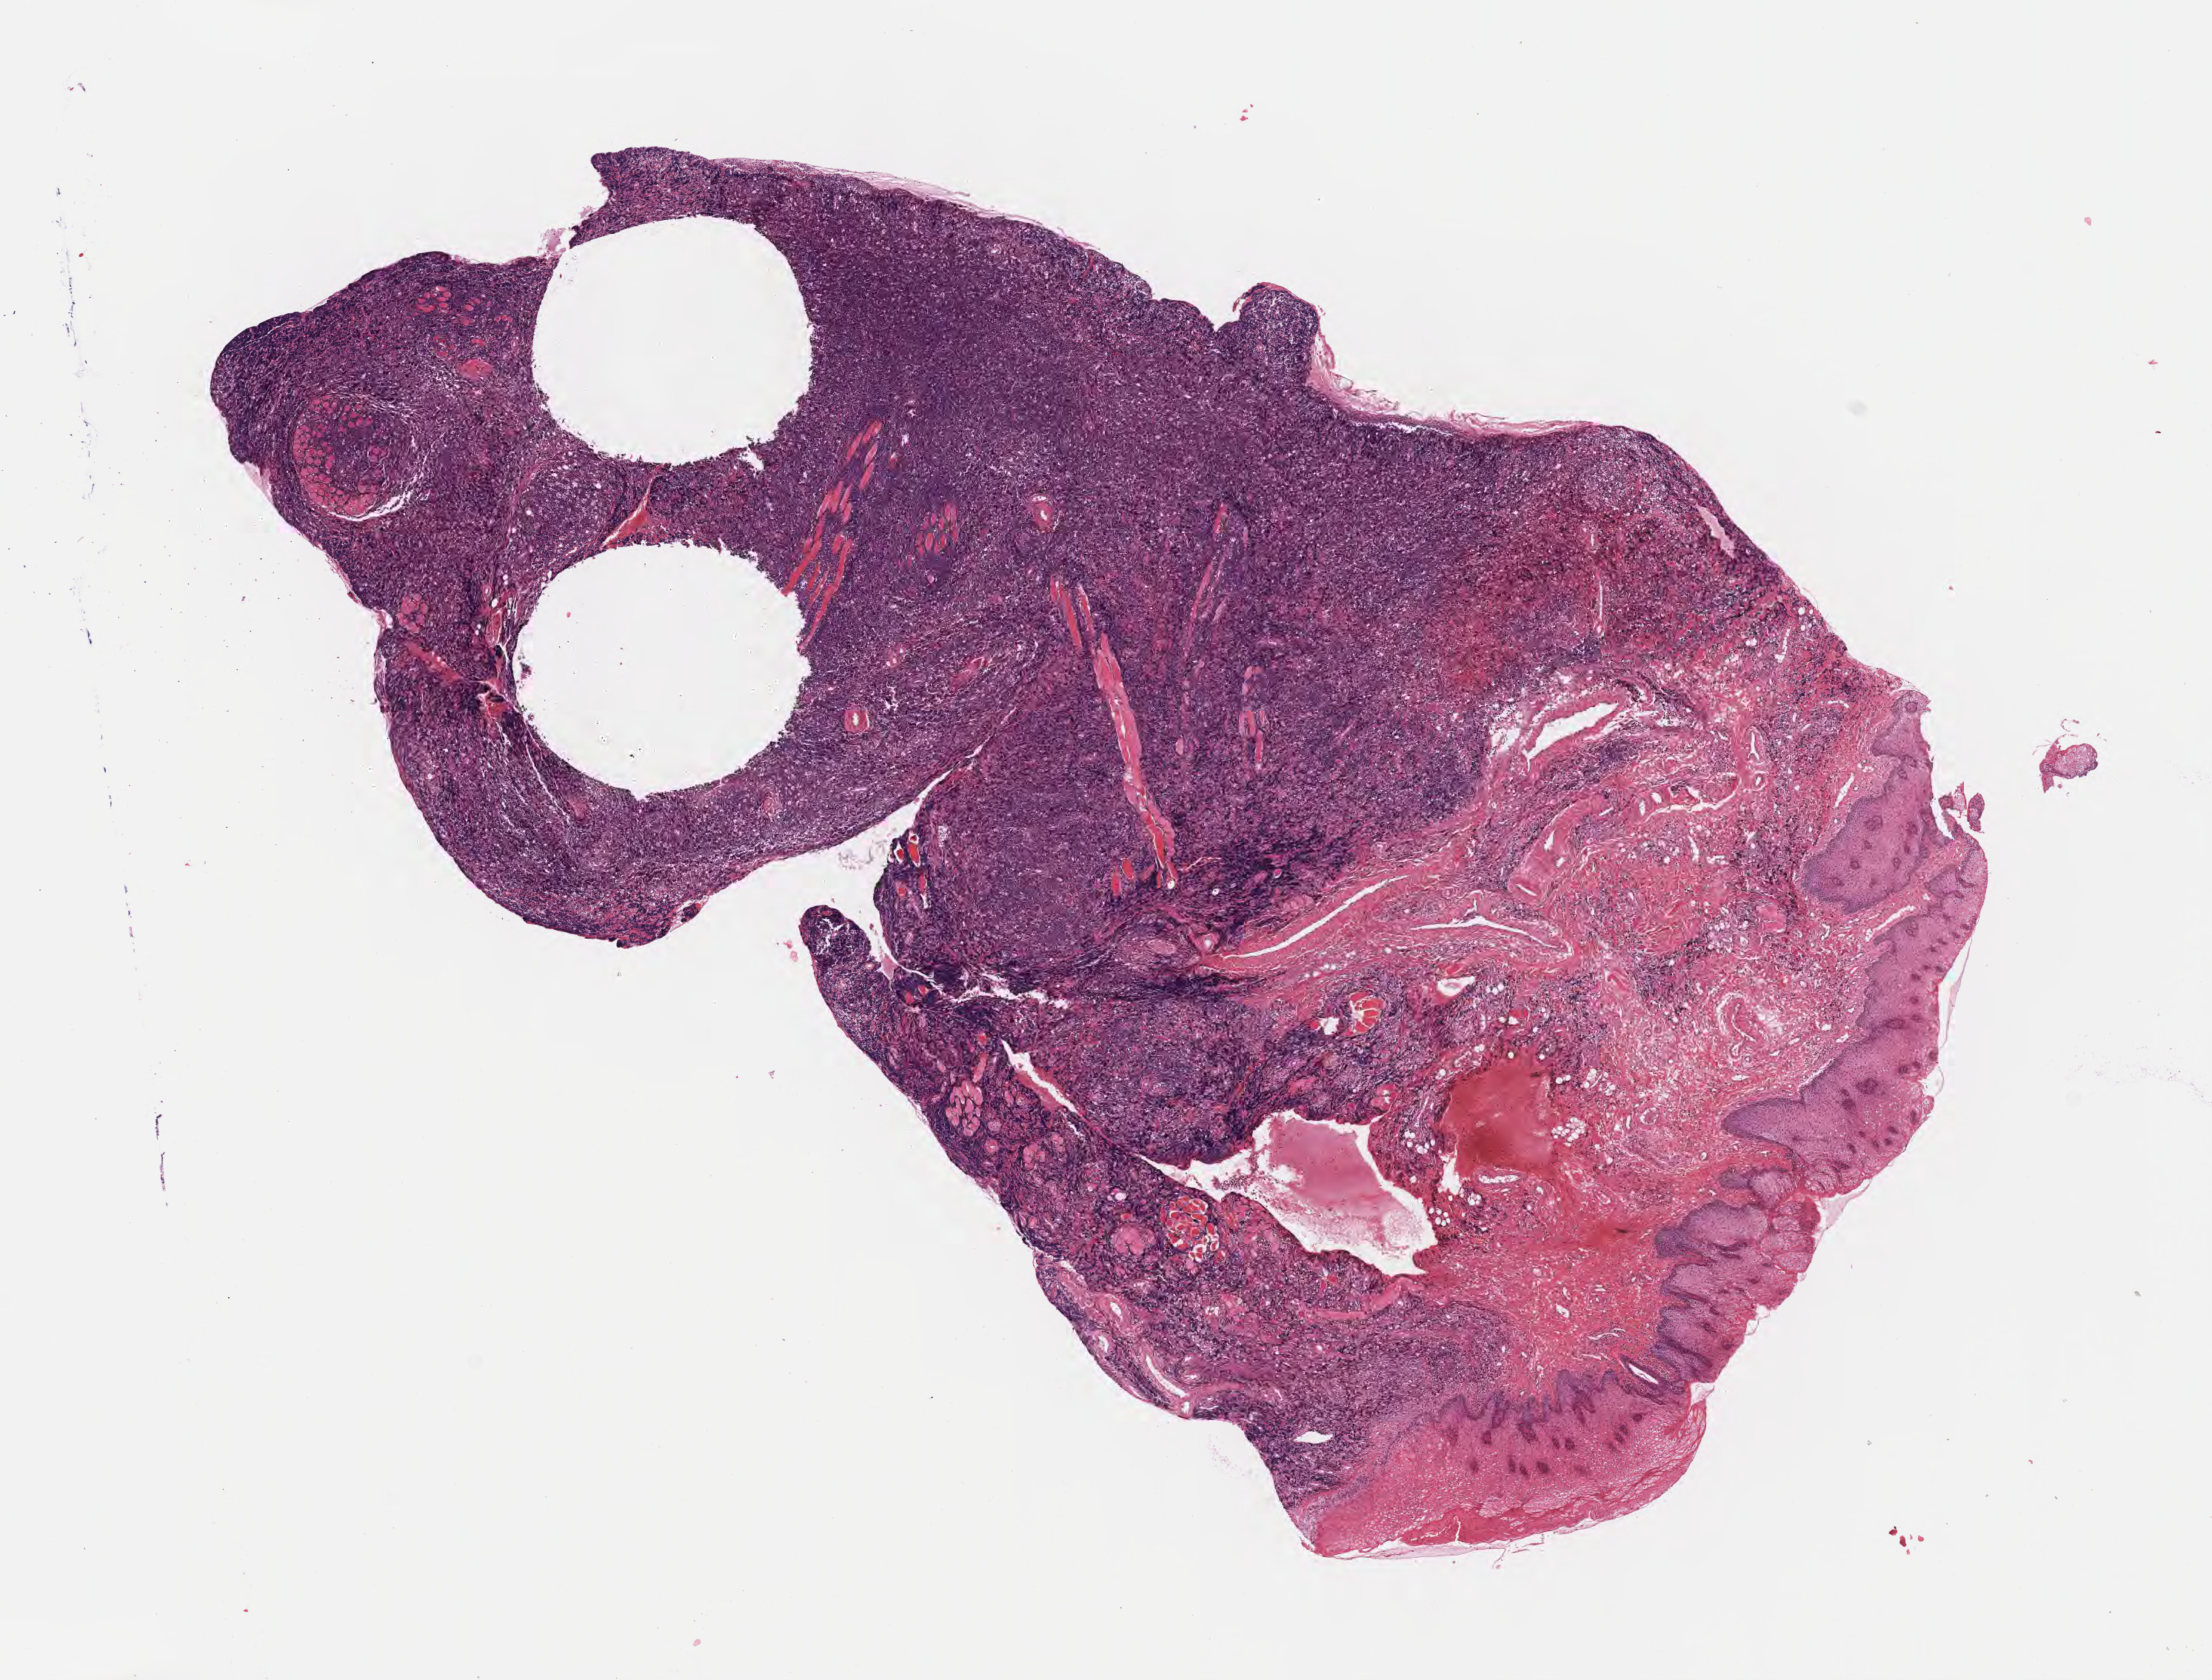
Digitized haematoxylin and eosin-stained section, whole scanned area (about 12.1 x 9.2 mm) shown as a low-resolution overview. Tumor tissue. Site: cranium. Male patient; age at initial diagnosis 6 years.
- histologic diagnosis: Burkitt lymphoma, NOS